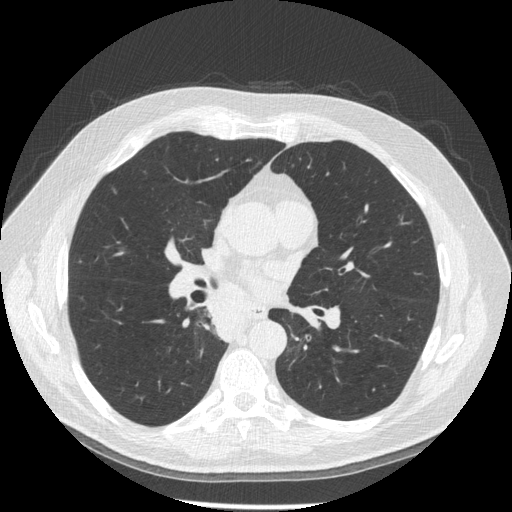
Axial slice from a low-dose chest CT screening exam, third screening round (two years after baseline), lung window (W 1500 / L -600 HU), 1.25 mm slice thickness, slice 85 of 181 in the series. Male, age 61 years at enrolment.
Lesion marked by an expert reader, bounding box [x1, y1, x2, y2] px = [204, 298, 256, 348]. No non-calcified nodule or mass ≥4 mm was recorded by the screening reader at this exam. Official screen result: positive, other. Later outcome: lung cancer diagnosed 10 days after this screen — squamous cell carcinoma, keratinizing, NOS, right lower lobe, stage IIIB (AJCC 6th edition), 40 mm at pathology.